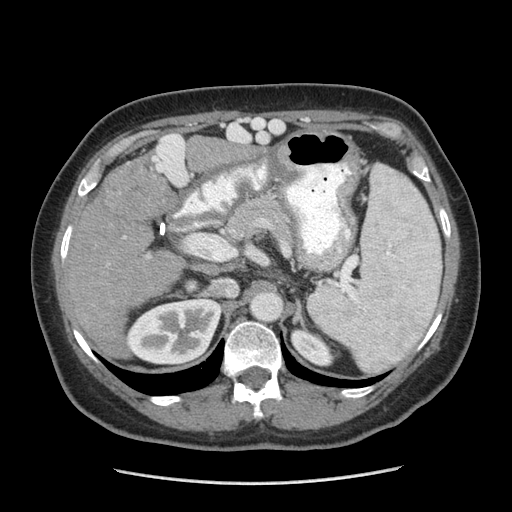
Contrast-enhanced abdominal CT (liver protocol), one axial slice; soft-tissue window (W 400 / L 40 HU); 512 × 512 image matrix, field of view 360 × 360 mm. Case-level facts recorded for this patient, not image findings: diagnosis: hepatocellular carcinoma (patient treated with transarterial chemoembolisation; whether this scan precedes or follows treatment is not stated here); TNM stage (as recorded): Stage-I; Child-Pugh class: A; tumour differentiation: poorly differentiated; tumour nodularity: uninodular.
Structures marked on this image (semi-automatic segmentation, software-assisted and operator-edited):
- liver parenchyma outside the tumour (the mass and vessels are separate outlines, so this box may not span the whole liver): bounding box <64,132,204,354> (left, top, right, bottom; pixels)
- mass: <102,159,171,221>
- liver vessels: <70,134,189,258>